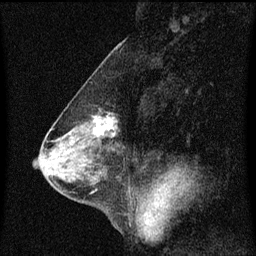
Breast MRI (dynamic contrast-enhanced), one sagittal slice. Position 32 of 60 along the scan axis. Dynamic contrast-enhanced series, image 2 of 3 at this slice position (ordered by acquisition). 1.5 T. TE 4.2 ms, TR 8.4 ms. 256 × 256 image matrix. Patient: female, 58 years.
Annotated regions visible in this slice (semi-automatically segmented with operator editing):
- analysis volume of interest (the breast-tissue region the enhancement analysis was run in; not a lesion): box from (x=79, y=108) to (x=120, y=143) px
- tumour enhancement mask (voxels above the 70 % enhancement threshold inside the analysis volume of interest): (x=94, y=116)–(x=118, y=137)